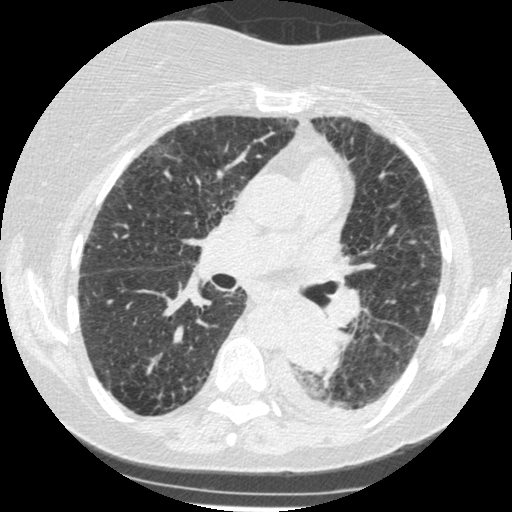
Low-dose screening chest CT, axial slice. Third annual screen. Lung window (W 1500 / L -600 HU). Slice 200 of 341 in the series. 512 × 512 image matrix. Female participant, aged 60 years at enrolment. Former smoker at enrolment.
Expert reader's lesion annotation, bounding box <271,307,342,374> (left, top, right, bottom; pixels). Reader record for this screening exam (exam-level; its link to the box is not recorded): non-calcified nodule or mass ≥4 mm, left lower lobe, 54 × 38 mm, smooth margins, soft tissue attenuation, pre-existing on the prior screen: yes; interval growth: yes.